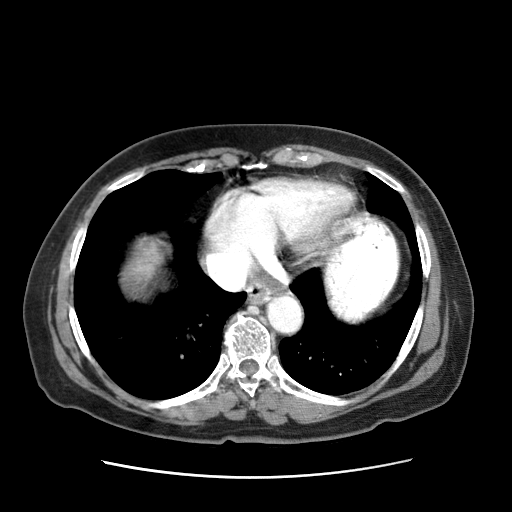
Contrast-enhanced abdominal CT (liver protocol), one axial slice. Slice 62 of 63 in the series (ordered by position). Reconstruction kernel STANDARD. Soft-tissue window (W 400 / L 40 HU). 512 × 512 image matrix. Female patient, age 79 years. From the clinical record (not read from this slice): diagnosis: hepatocellular carcinoma (patient treated with transarterial chemoembolisation; whether this scan precedes or follows treatment is not stated here); TNM stage (as recorded): Stage-II; Child-Pugh class: B; tumour differentiation: well differentiated; tumour nodularity: multinodular.
Structures marked on this image (semi-automatic segmentation, software-assisted and operator-edited):
- abdominal aorta: bounding box (x1, y1, x2, y2) in pixels: (266, 295, 301, 333)
- liver parenchyma outside the tumour (the mass and vessels are separate outlines, so this box may not span the whole liver): (116, 236, 317, 302)